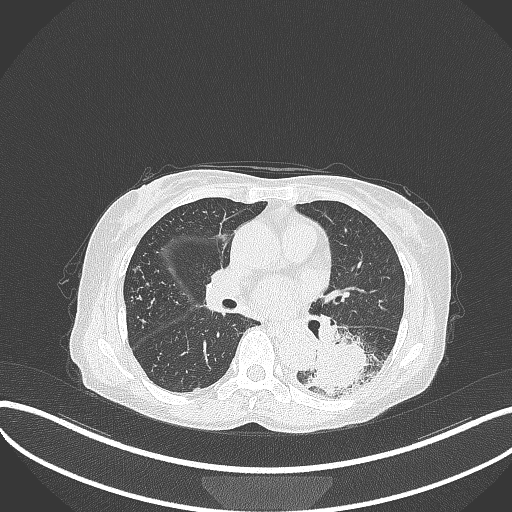
Chest CT, one axial slice; slice 165 of 370 in the series (ordered by position); reconstruction kernel B70f; 120 kVp; lung window (W 1500 / L -600 HU); 1 mm slice thickness; 512 × 512 image matrix. Female patient, age 78 years. Case-level facts recorded for this patient, not image findings: clinical TNM (as recorded): T3 N0 M1.
Annotated regions visible in this slice (bounding box drawn by a radiologist):
- lung tumour (recorded histology: squamous cell carcinoma): bounding box <302,342,378,396> (left, top, right, bottom; pixels)